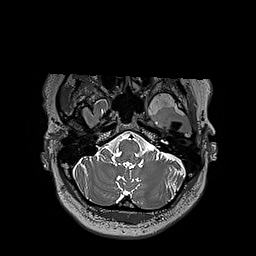
Brain MRI from a brain-tumour surgery series, one axial slice; slice 156 of 192 in the series (ordered by position); 1 mm slice thickness; 256 × 256 image matrix, field of view 250 × 250 mm. Case-level facts recorded for this patient, not image findings: histopathology: Oligodendroglioma; WHO grade: 3; IDH mutation: yes; tumour location: Left Sylvian Fissure (Temporal).
Outlined on this slice (outlined manually by an expert reader):
- tumour: bounding box <124,92,197,113> (left, top, right, bottom; pixels)